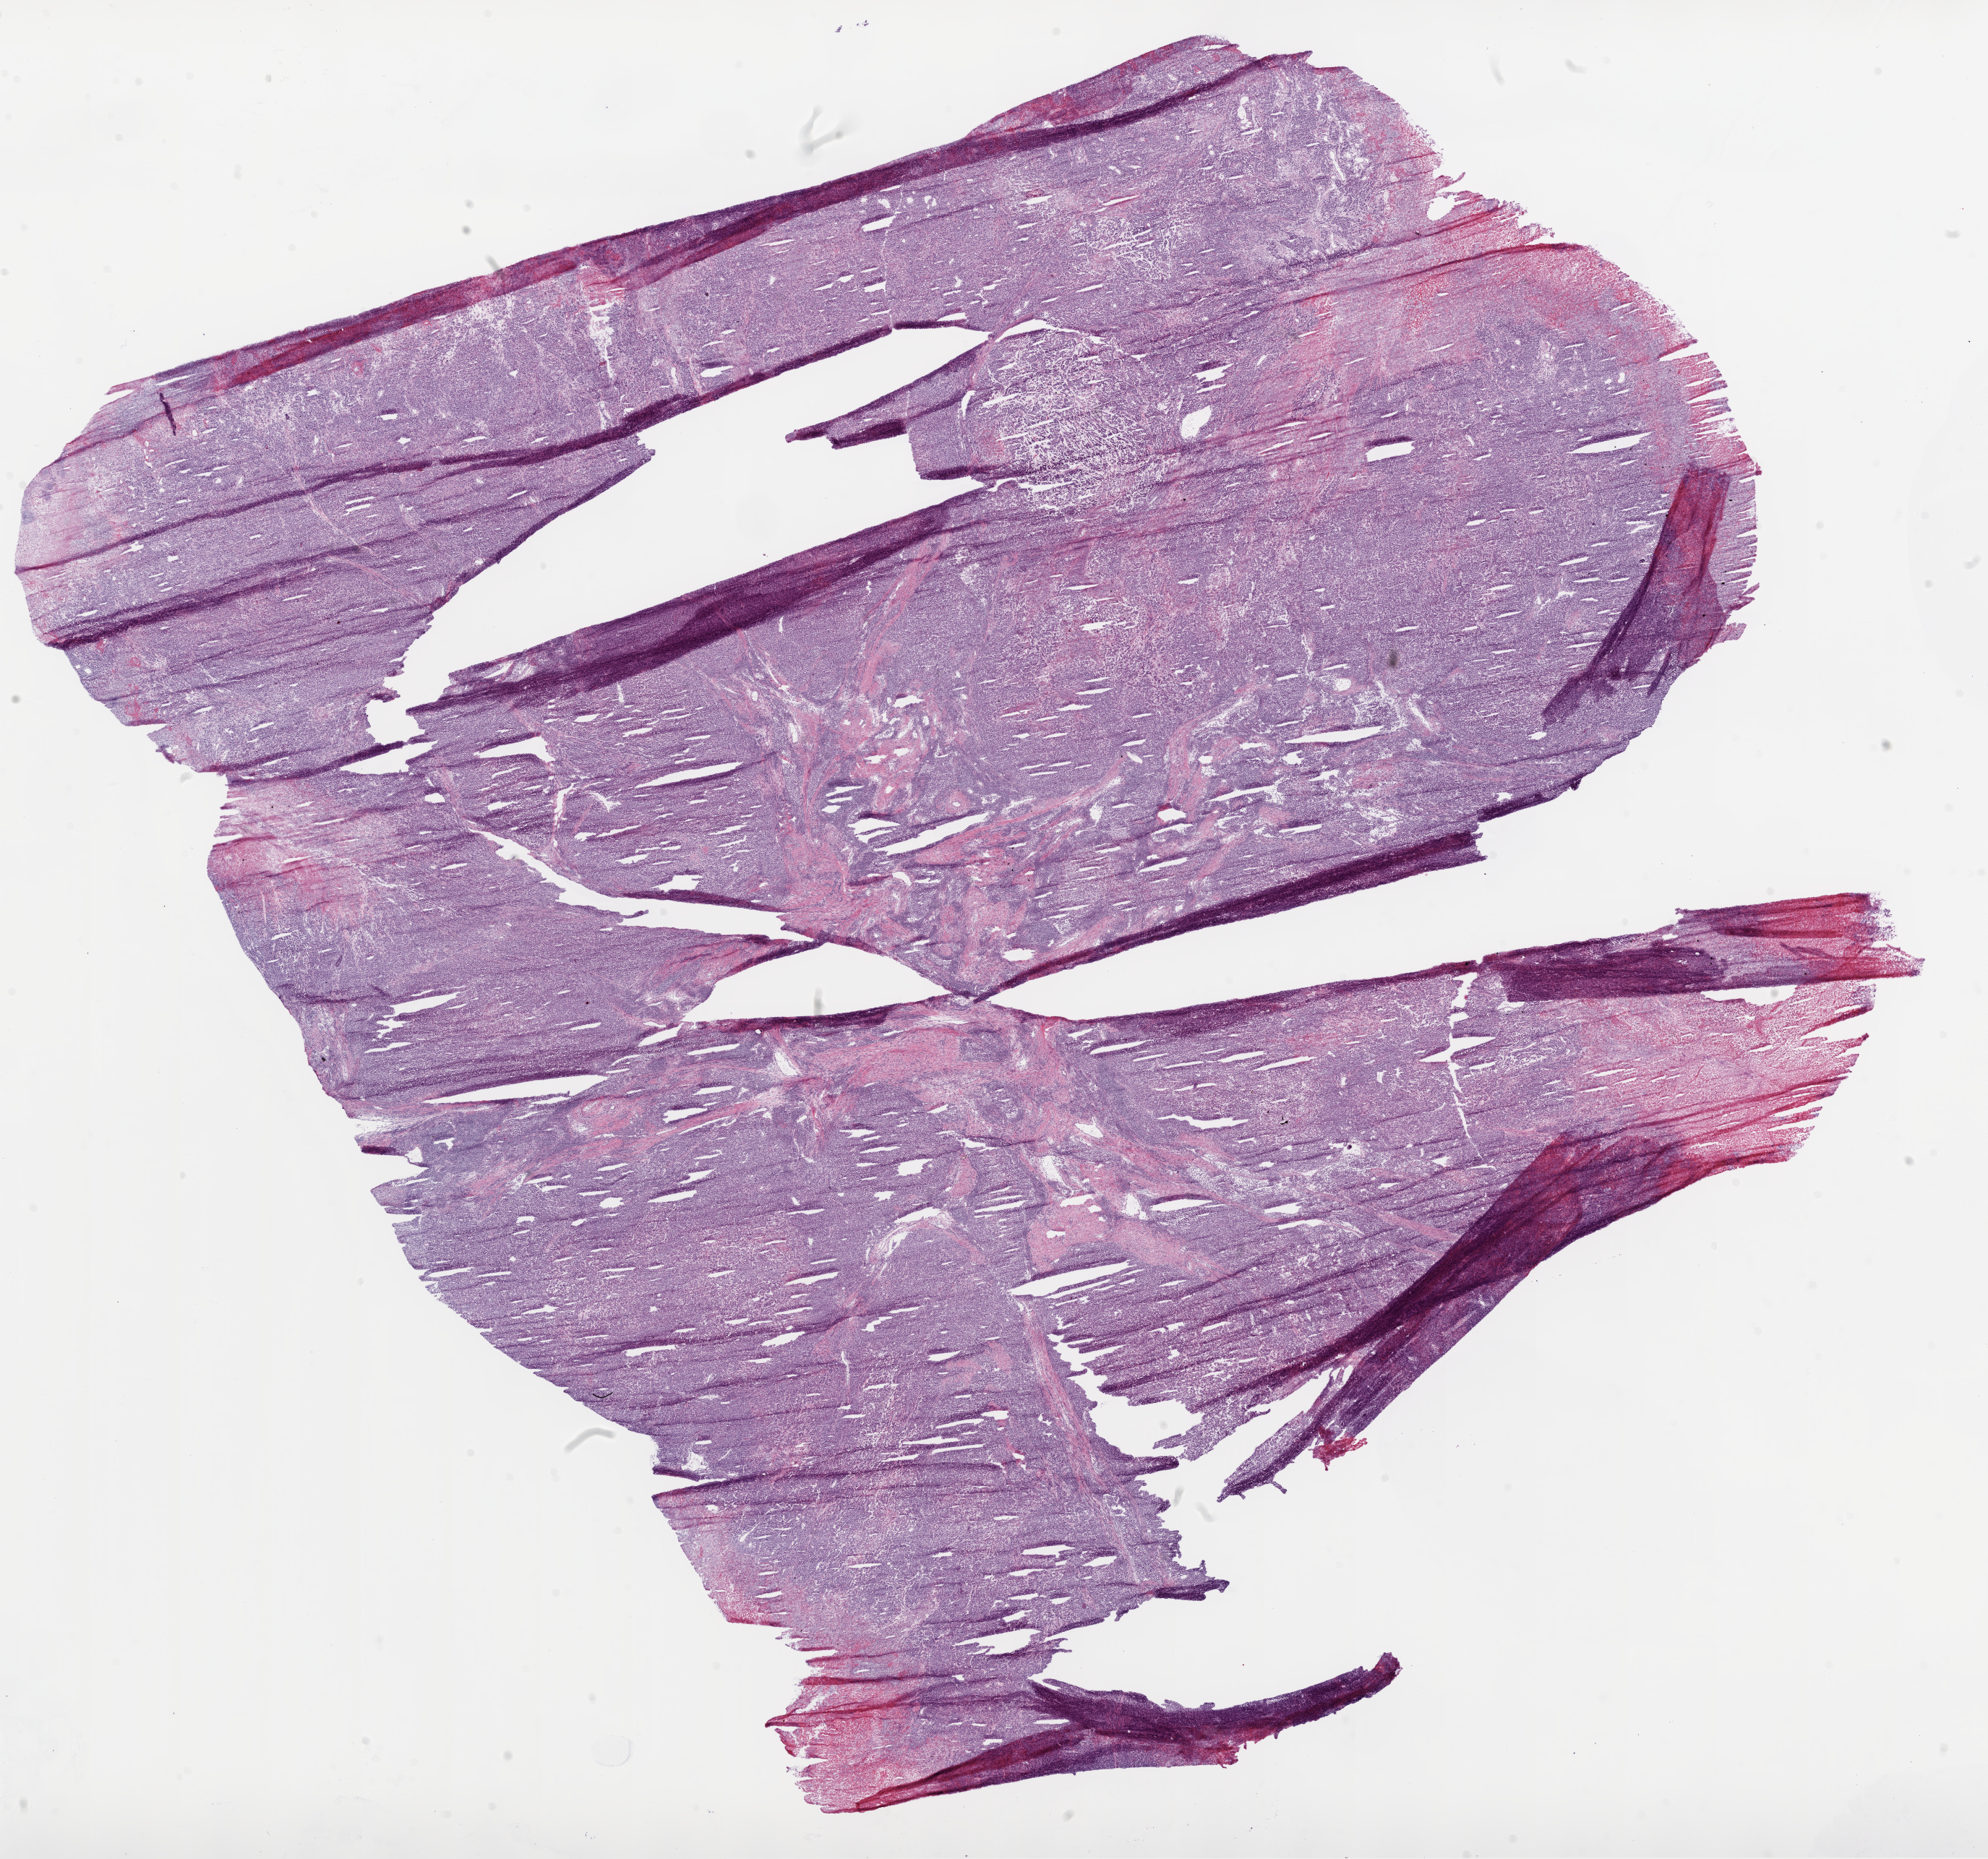
Digitized H&E tissue section (whole slide) — low-resolution overview of the scanned area, about 22.1 x 20.6 mm, frozen section, stomach, primary tumour sample. Patient: female, age at initial diagnosis 74 years. Histologic grade: G3 (poorly differentiated). Composition of this section per pathologist review: tumour cells 85%, tumour nuclei 80%, normal cells 0%, stromal cells 5%, necrosis 10%.
• pathologic diagnosis: Adenocarcinoma, NOS